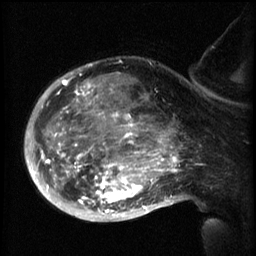
Breast MRI (dynamic contrast-enhanced), one sagittal slice. Position 43 of 60 along the scan axis. 3 images stored at this slice position (order not interpretable as contrast timing). 1.5 T. TE 4.2 ms, TR 8.2 ms. 2.3 mm slice thickness. 256 × 256 image matrix. Patient: female, 50 years.
Structures marked on this image (semi-automatically segmented with operator editing):
- analysis volume of interest (the breast-tissue region the enhancement analysis was run in; not a lesion): bounding box (x1, y1, x2, y2) in pixels: (50, 66, 169, 217)
- tumour enhancement mask (voxels above the 70 % enhancement threshold inside the analysis volume of interest): (50, 74, 169, 217)